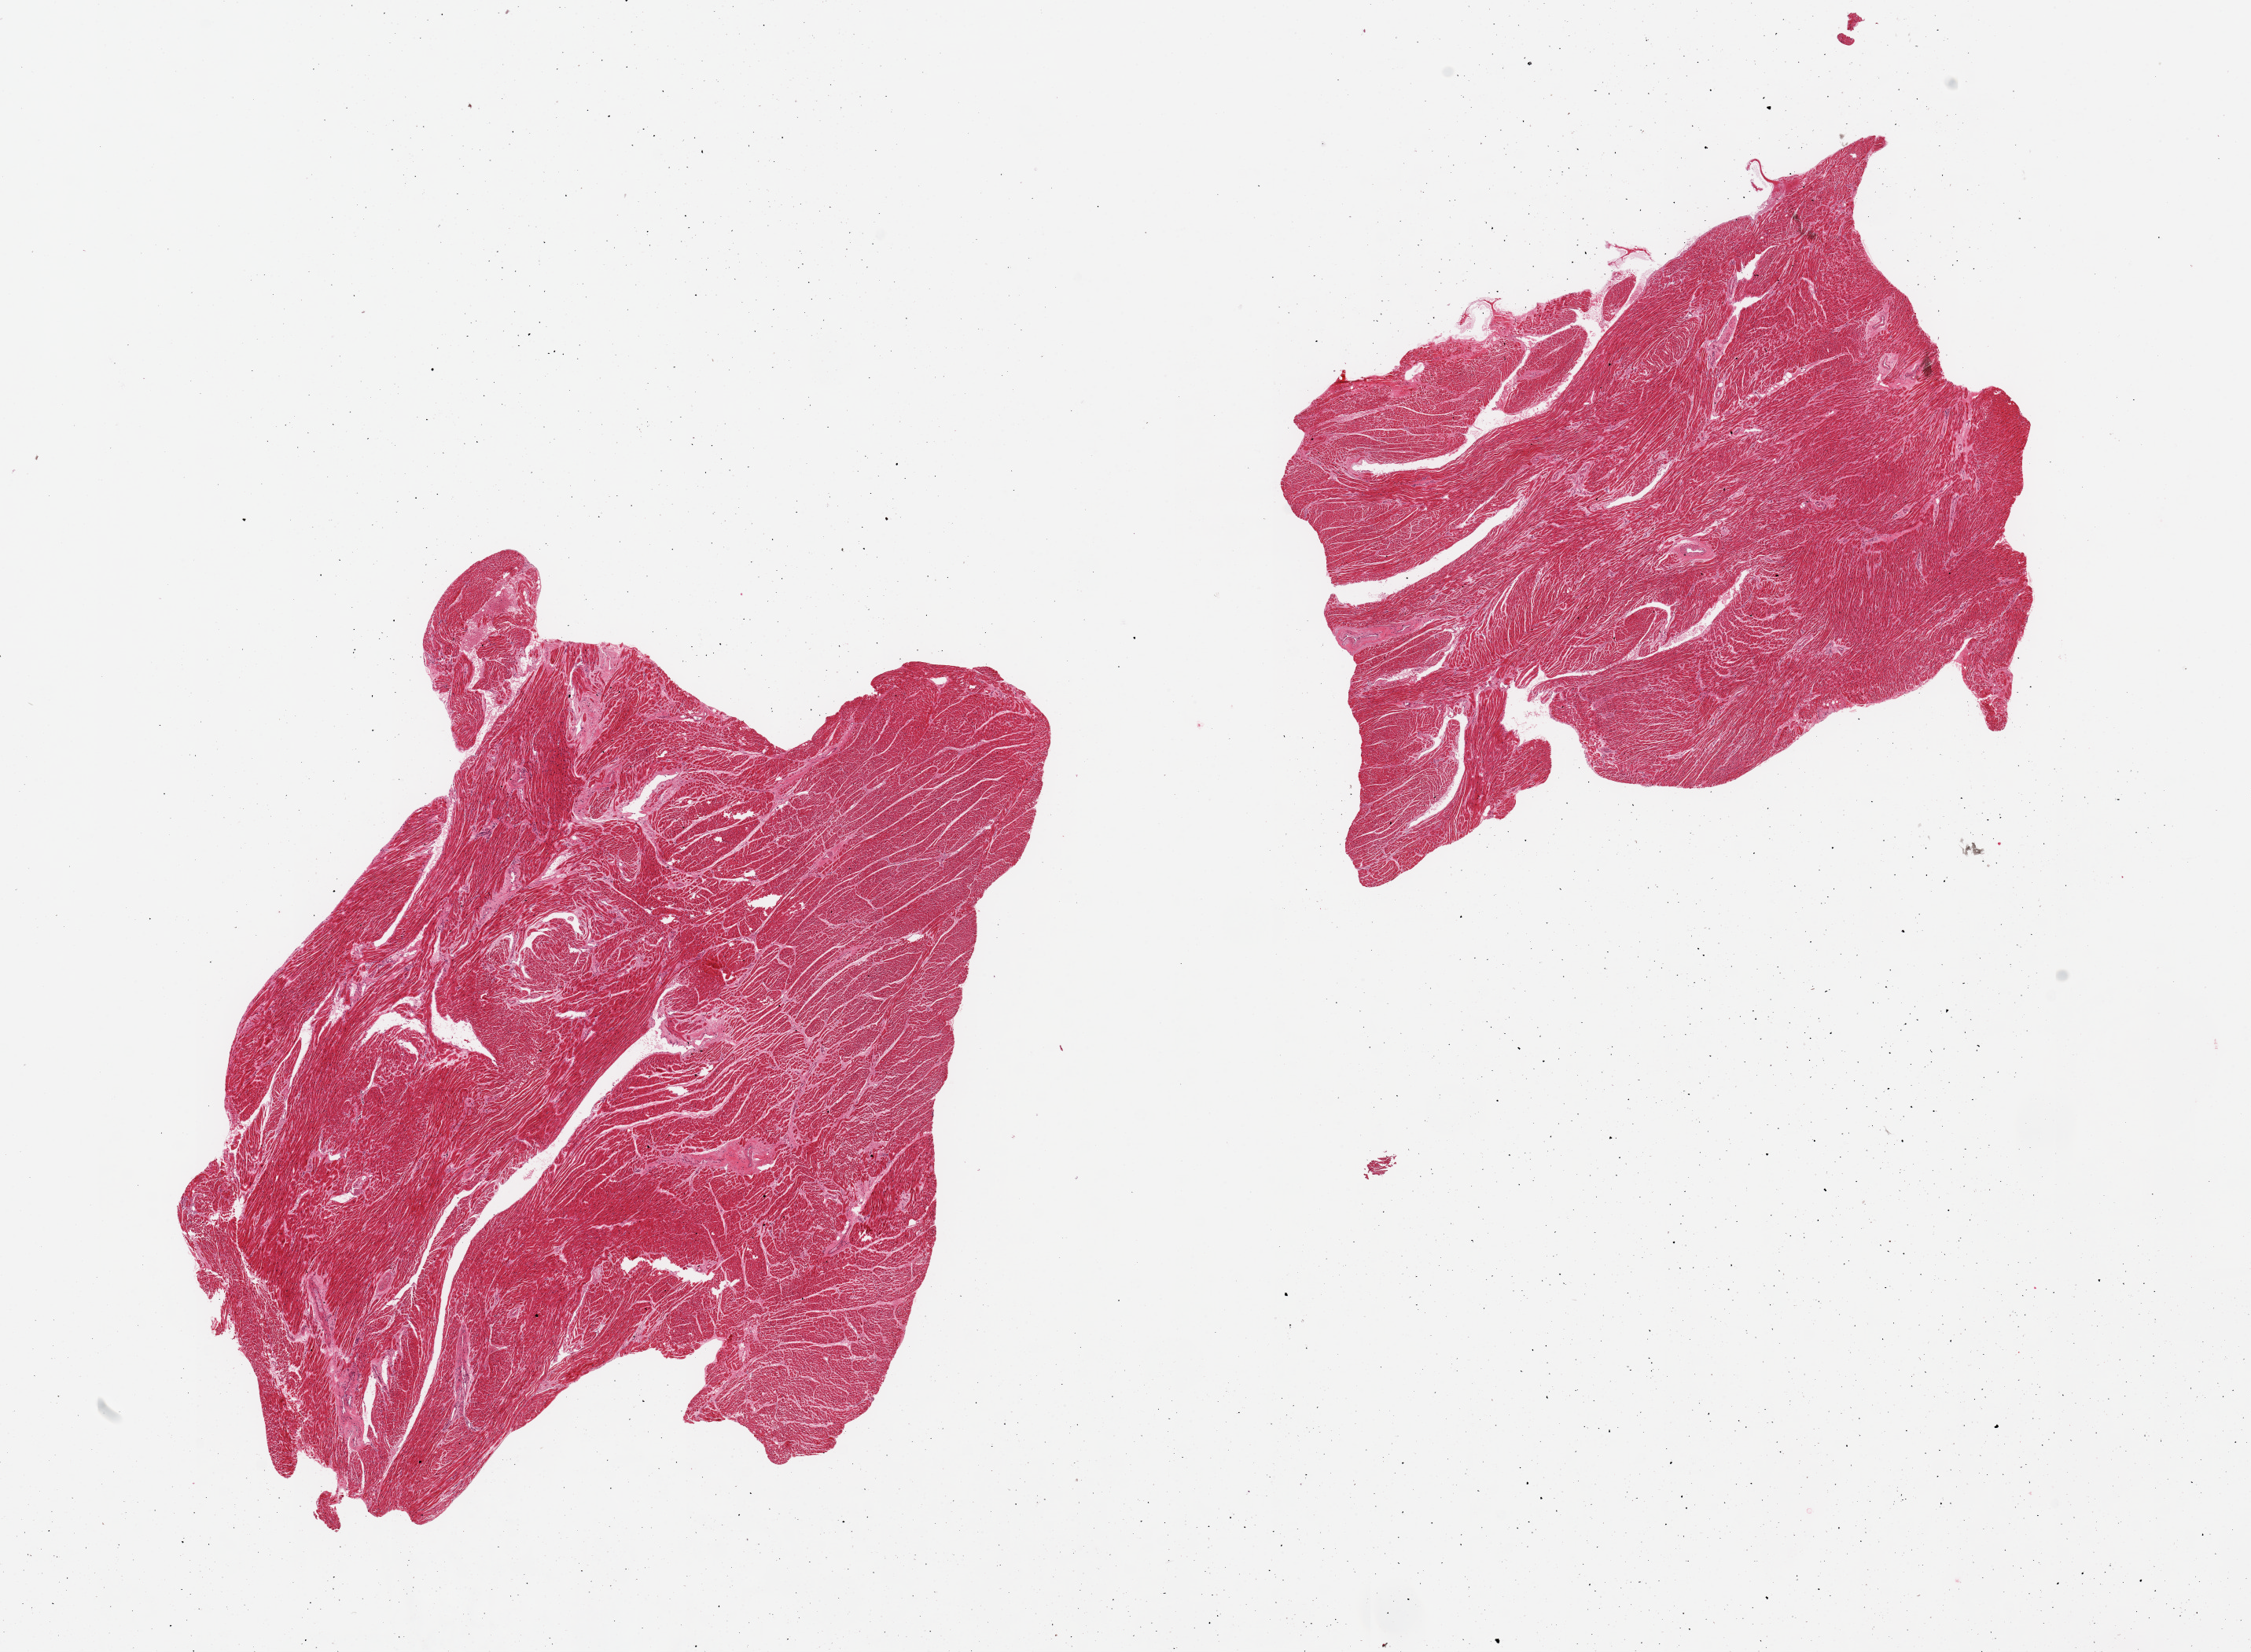
Digitized hematoxylin and eosin (H&E)-stained section, shown as a low-resolution overview of the whole scanned area (about 22.6 x 16.6 mm). PAXgene-fixed, paraffin-embedded tissue. Target tissue: heart. Tissue donor sample. Donor: female.
* reviewer comment on this tissue sample: 2 pieces